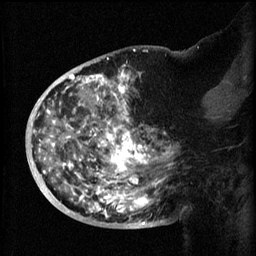
Breast MRI (dynamic contrast-enhanced), one sagittal slice. Position 31 of 60 along the scan axis. 3 images stored at this slice position (order not interpretable as contrast timing). 1.5 T. TE 4.2 ms, TR 8.2 ms. 256 × 256 image matrix. Female patient, age 50 years.
Outlined on this slice (semi-automatic segmentation, software-assisted and operator-edited):
- analysis volume of interest (the breast-tissue region the enhancement analysis was run in; not a lesion): box from (x=44, y=72) to (x=173, y=219) px
- tumour enhancement mask (voxels above the 70 % enhancement threshold inside the analysis volume of interest): (x=44, y=72)–(x=170, y=219)